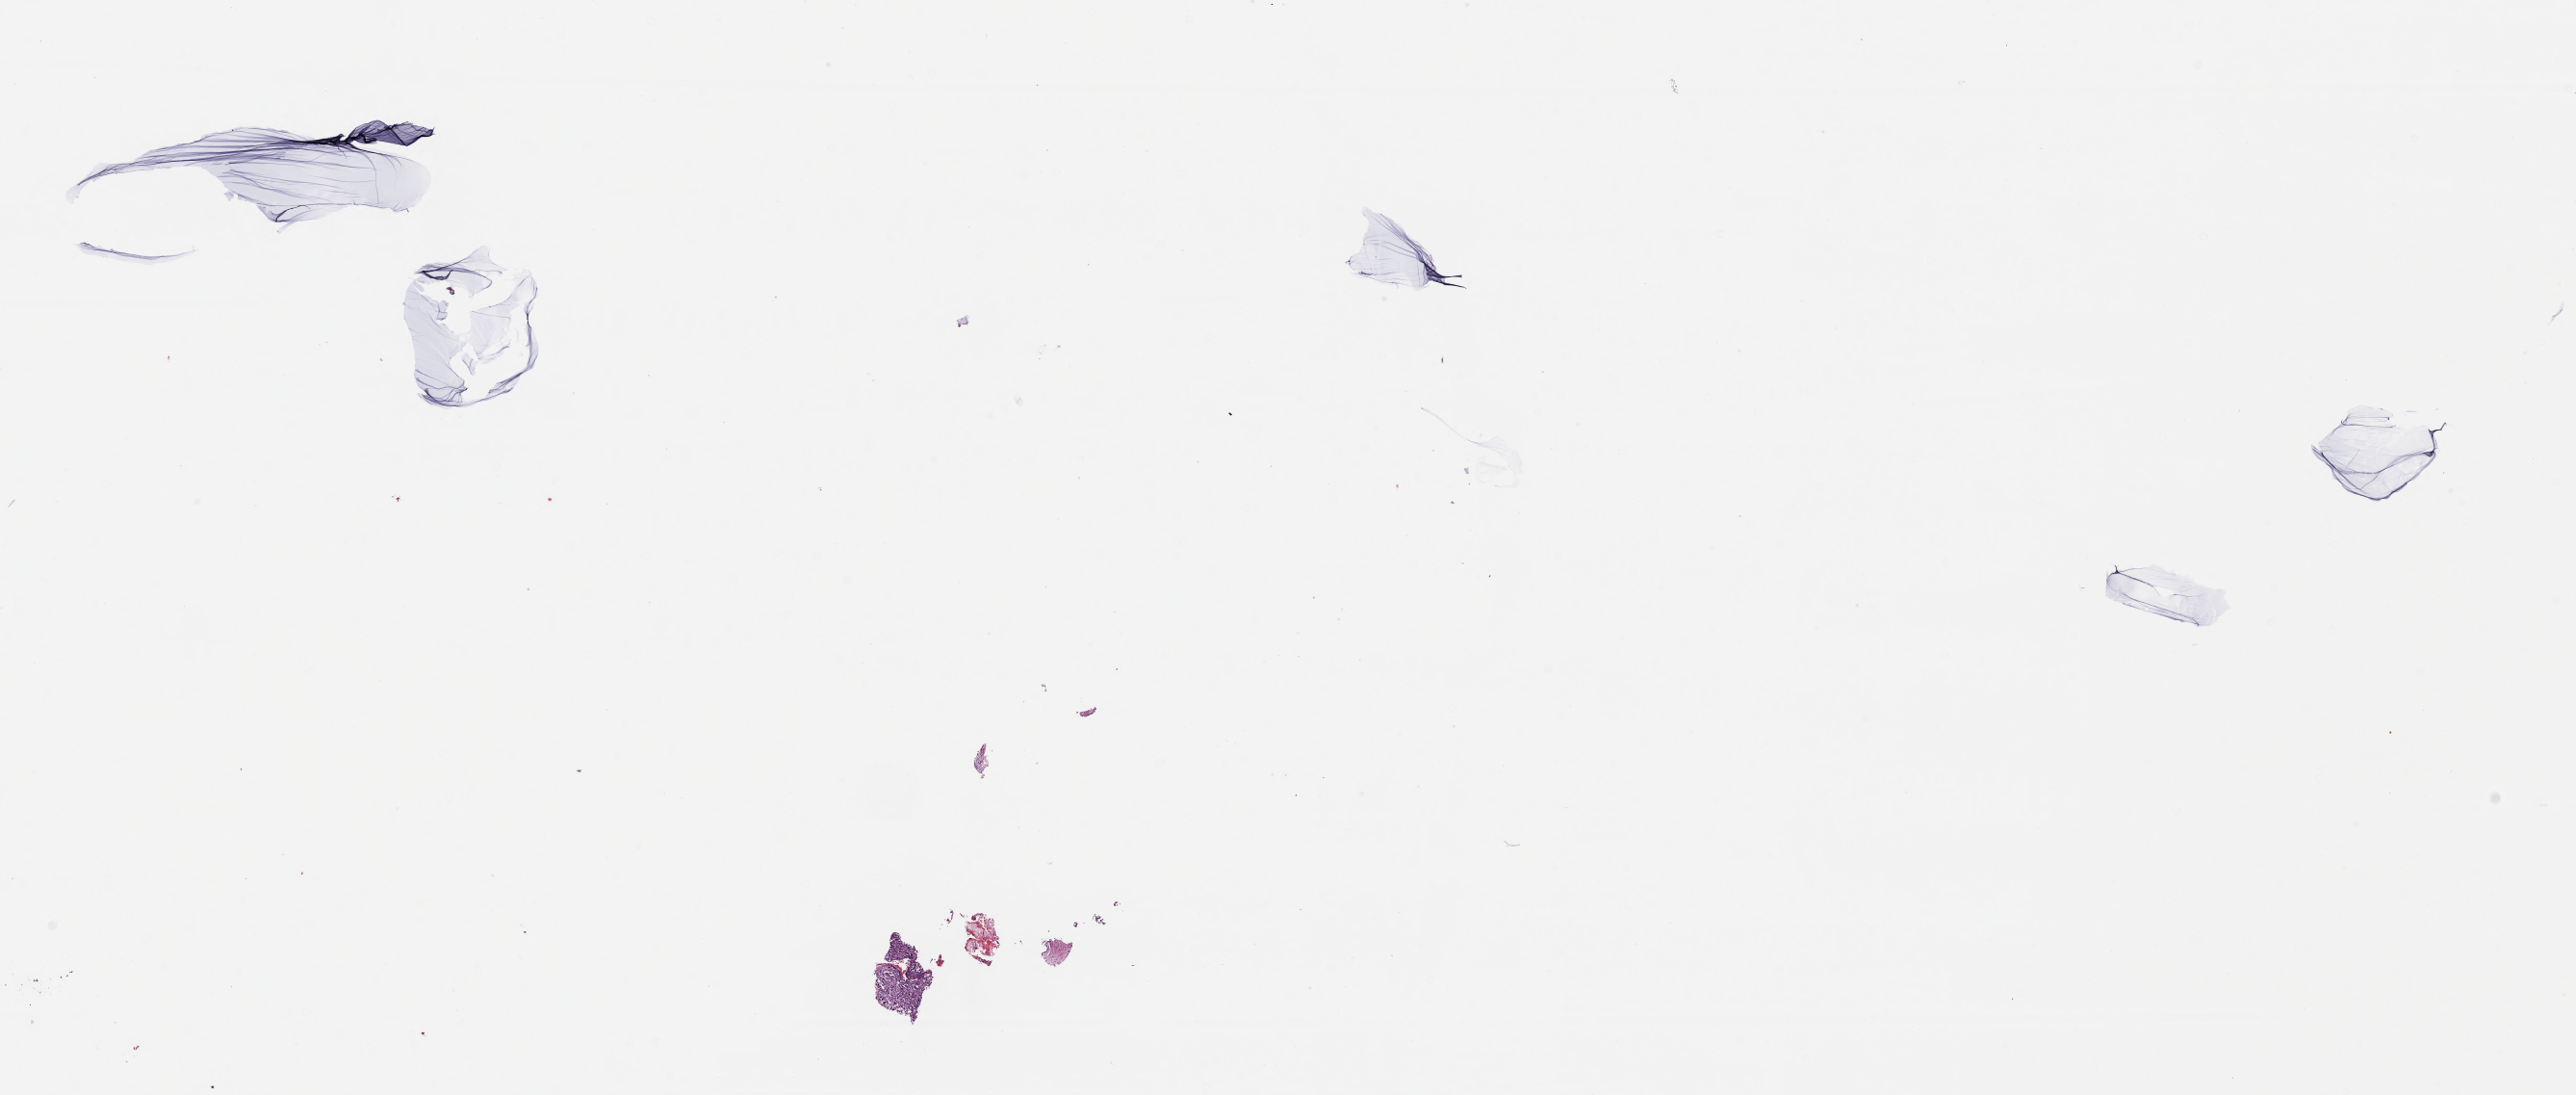
Digitized H&E-stained section, low-resolution overview of the scanned area, about 21.6 x 9.2 mm; specimen: tumor tissue; site: lung (right). Patient male; aged 63.
- histologic diagnosis: Adenocarcinoma, NOS